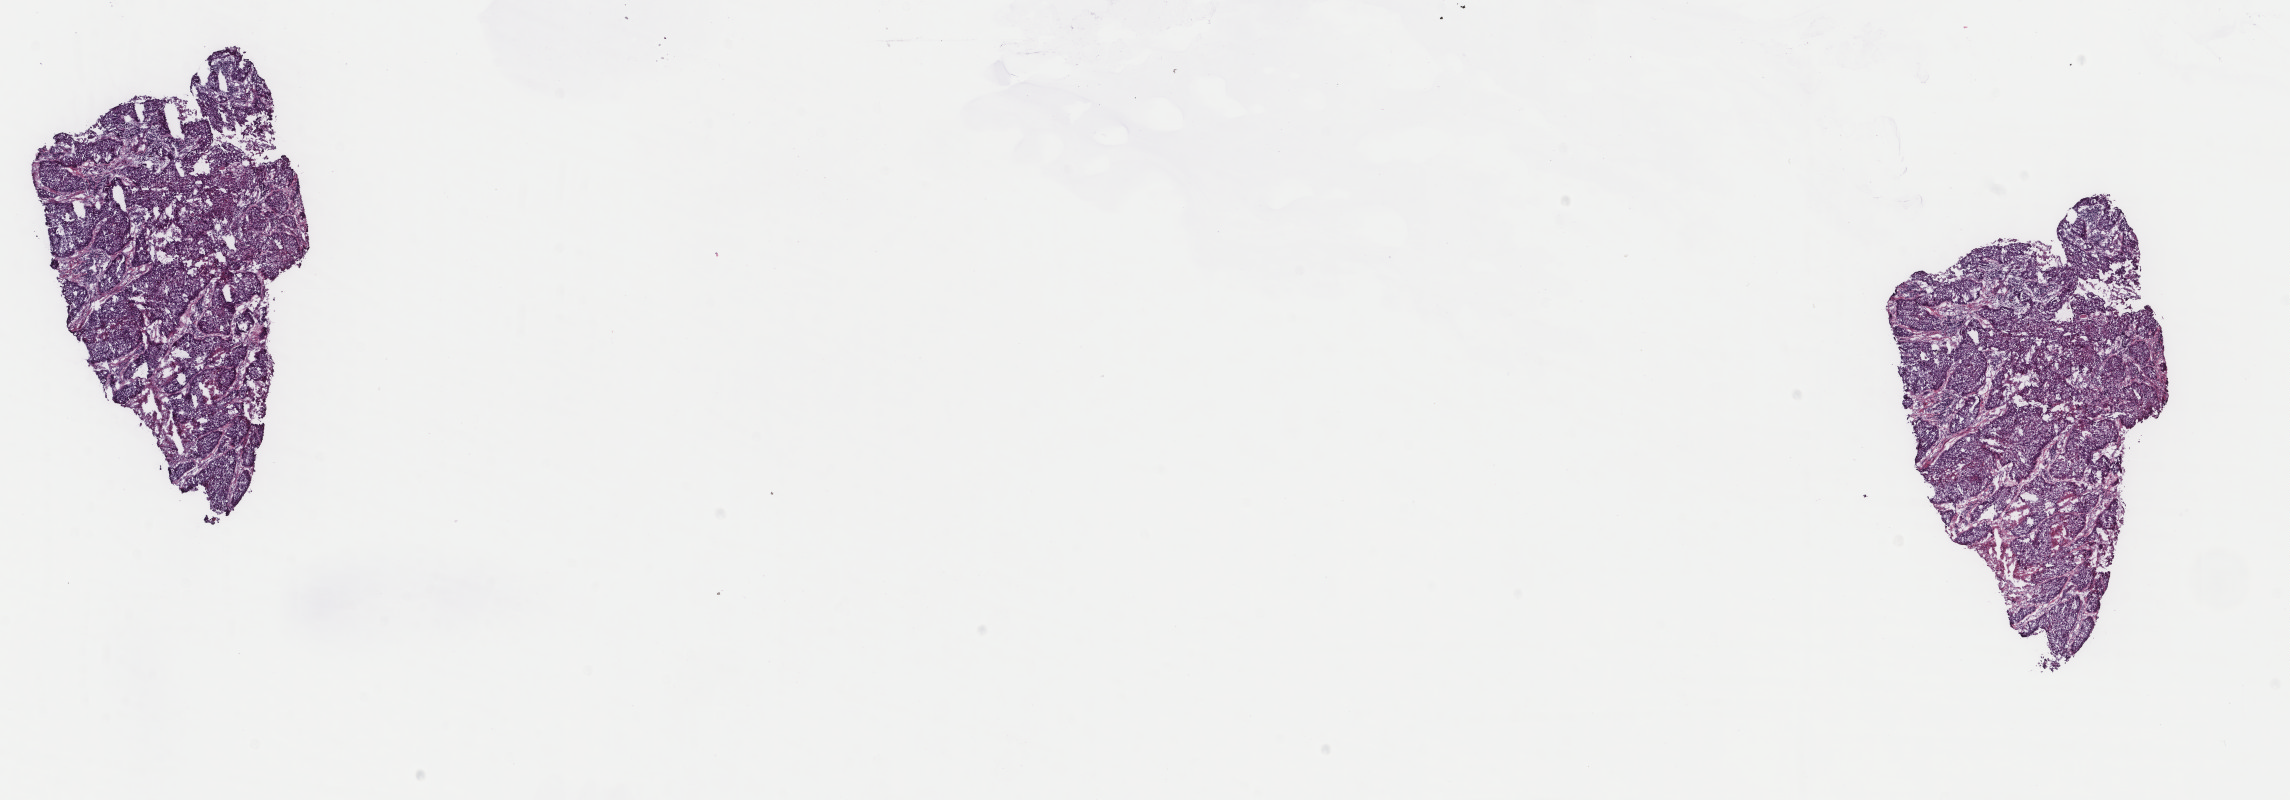
Whole-slide histology image, H&E — shown as a low-resolution overview of the whole scanned area (about 18.2 x 6.4 mm, from a 40x scan). Frozen section from the top of the tissue portion. Sample: primary tumour, lung. Male, age 65 years at initial diagnosis. Composition of this section per pathologist review: tumour cells 85%, tumour nuclei 90%, normal cells 0%, stromal cells 15%, necrosis 0%. Infiltration values recorded for this section: lymphocyte infiltration 0%, monocyte infiltration 0%, neutrophil infiltration 0%.
• histologic diagnosis: Squamous cell carcinoma, NOS
• AJCC pathologic stage: IIIA (6th edition)
• TNM: T2 N2 M0